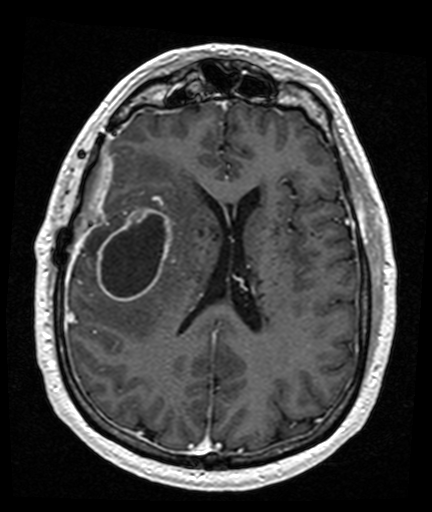
Brain MRI from a brain-tumour surgery series, one axial slice; slice 68 of 176 in the series (ordered by position); T1-weighted post-contrast; 1 mm slice thickness; 432 × 512 image matrix, field of view 194 × 230 mm. From the clinical record (not read from this slice): histopathology: Glioblastoma; WHO grade: 4; IDH mutation: no; tumour location: Right Frontal Temporal, Posterior Sylvian Fissure.
Annotated regions visible in this slice (manually delineated by an expert):
- tumour: box from (x=97, y=207) to (x=173, y=302) px